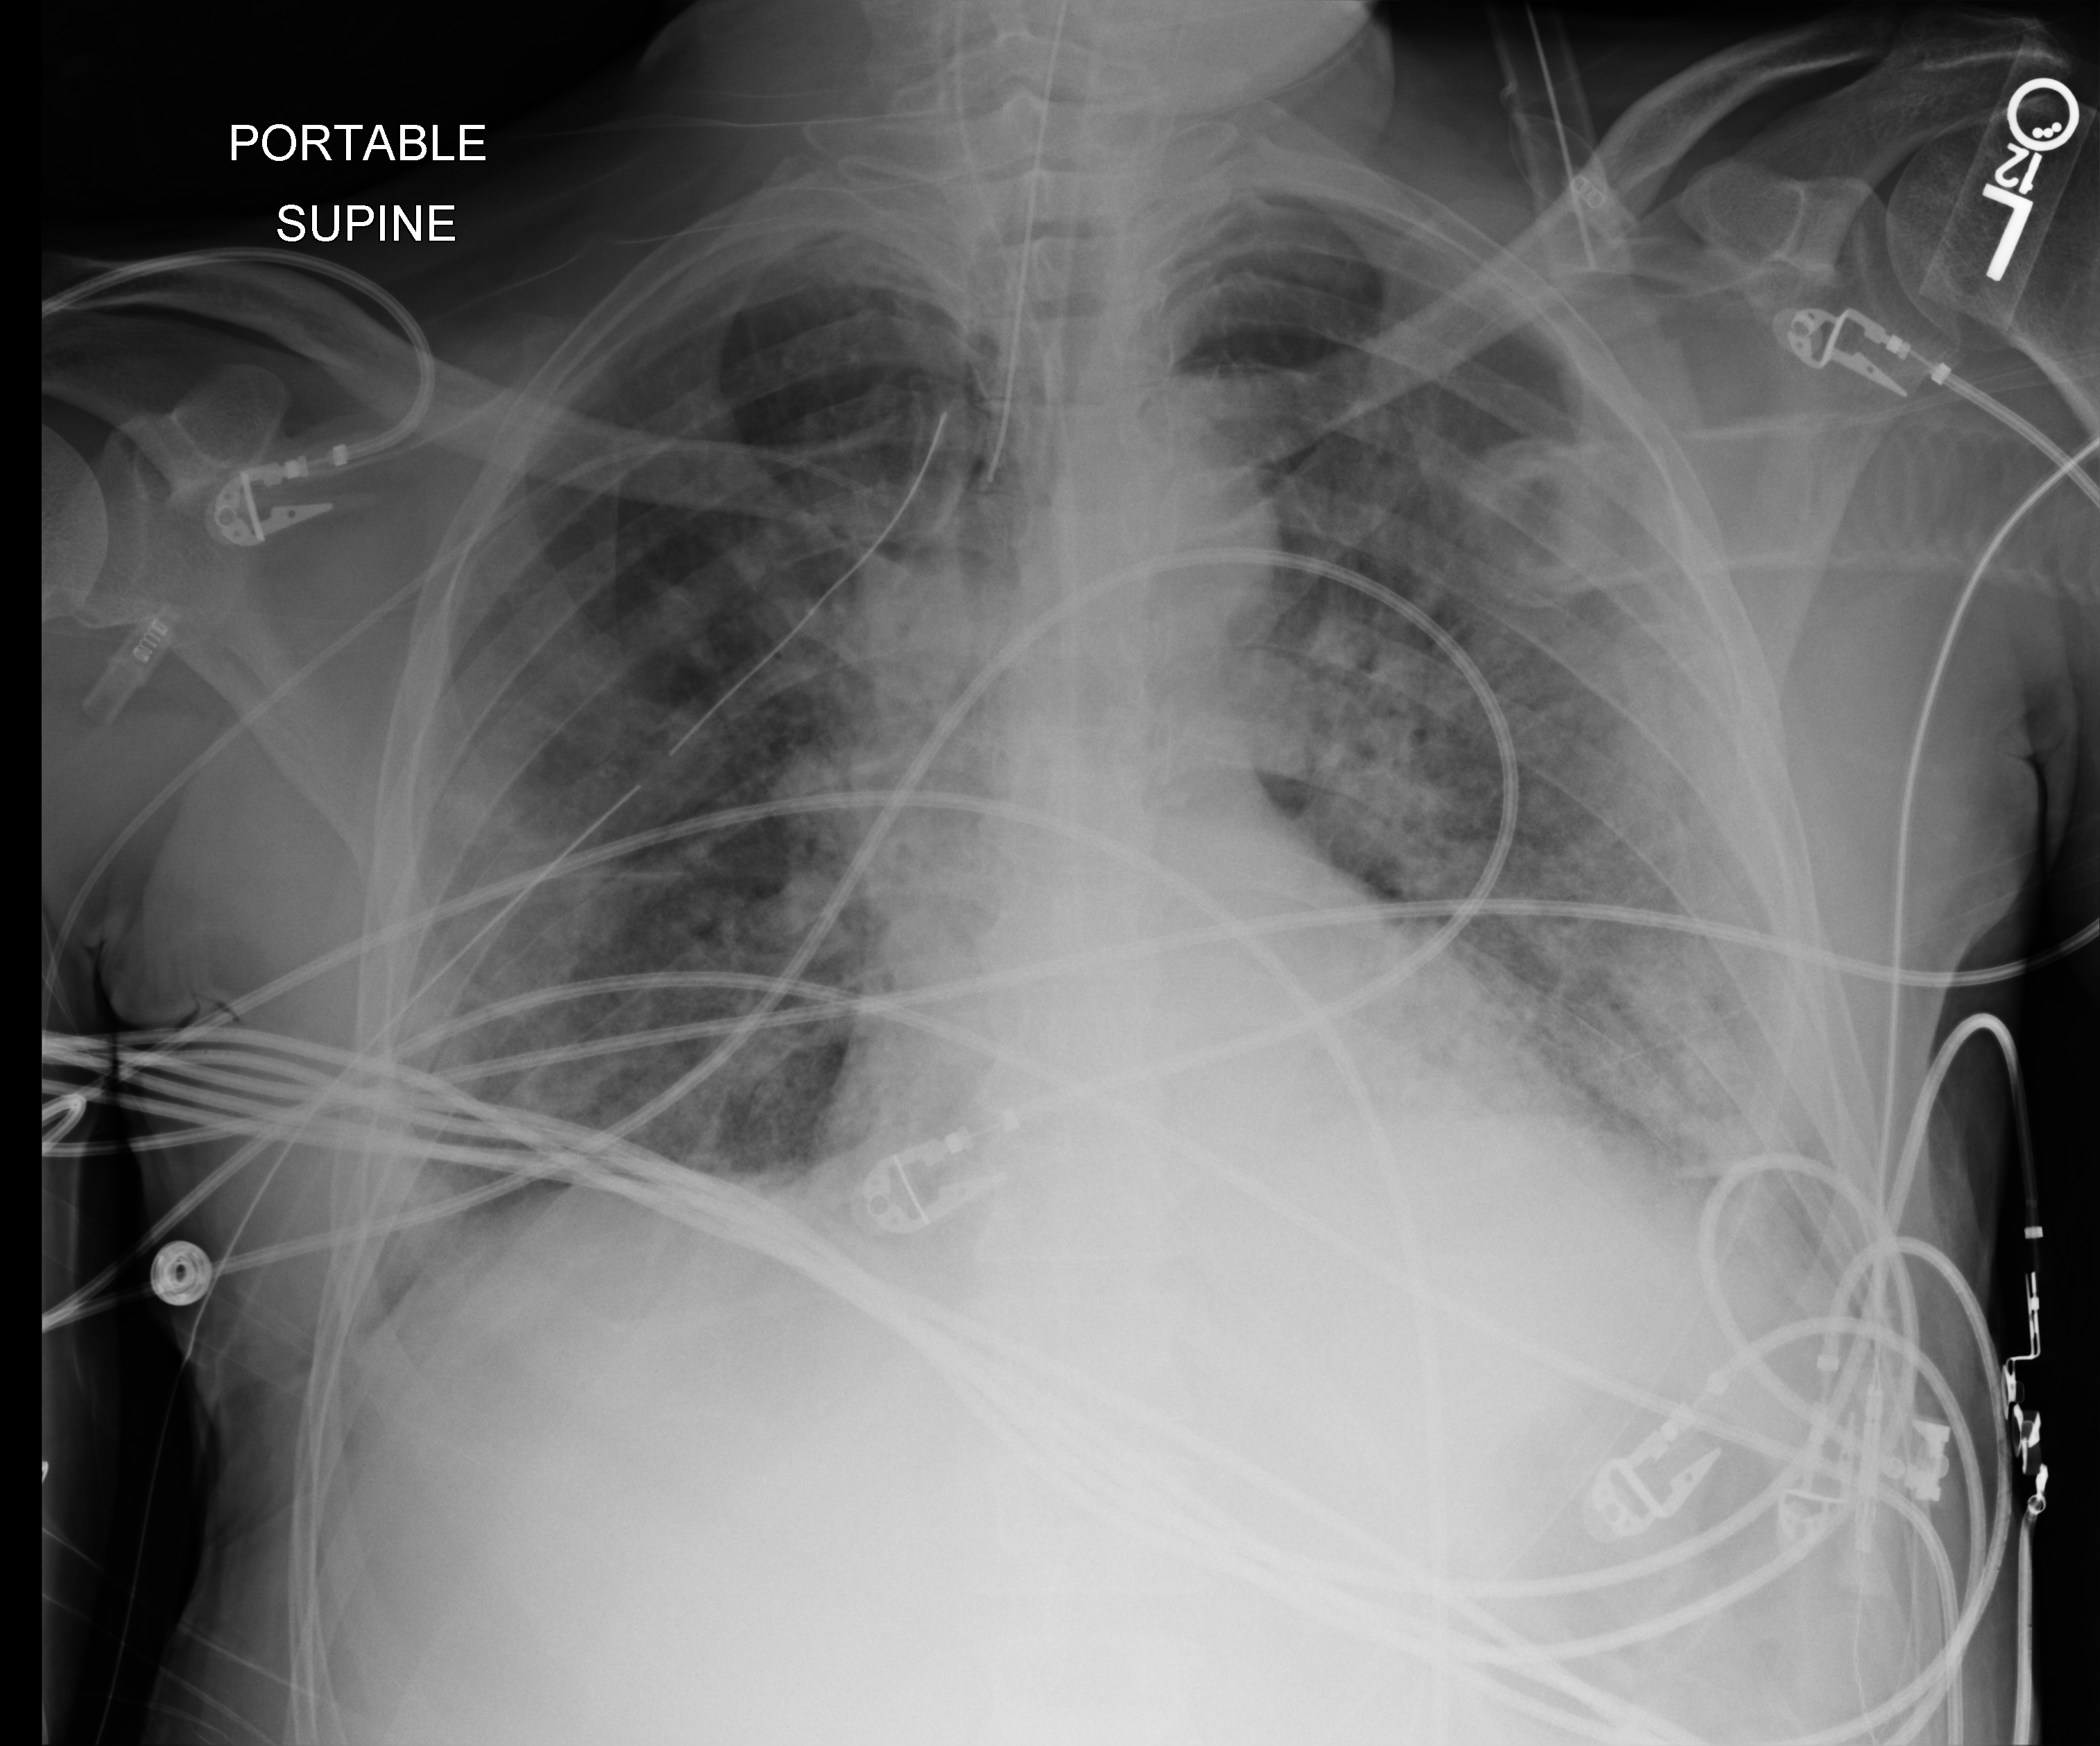
Portable chest radiograph, anteroposterior (AP) projection. Patient hospitalised with COVID-19; male, aged 18–59 years.
Hospital-stay facts (about this admission, not read from this image; timing relative to this image not recorded): length of hospital stay: 41 days.